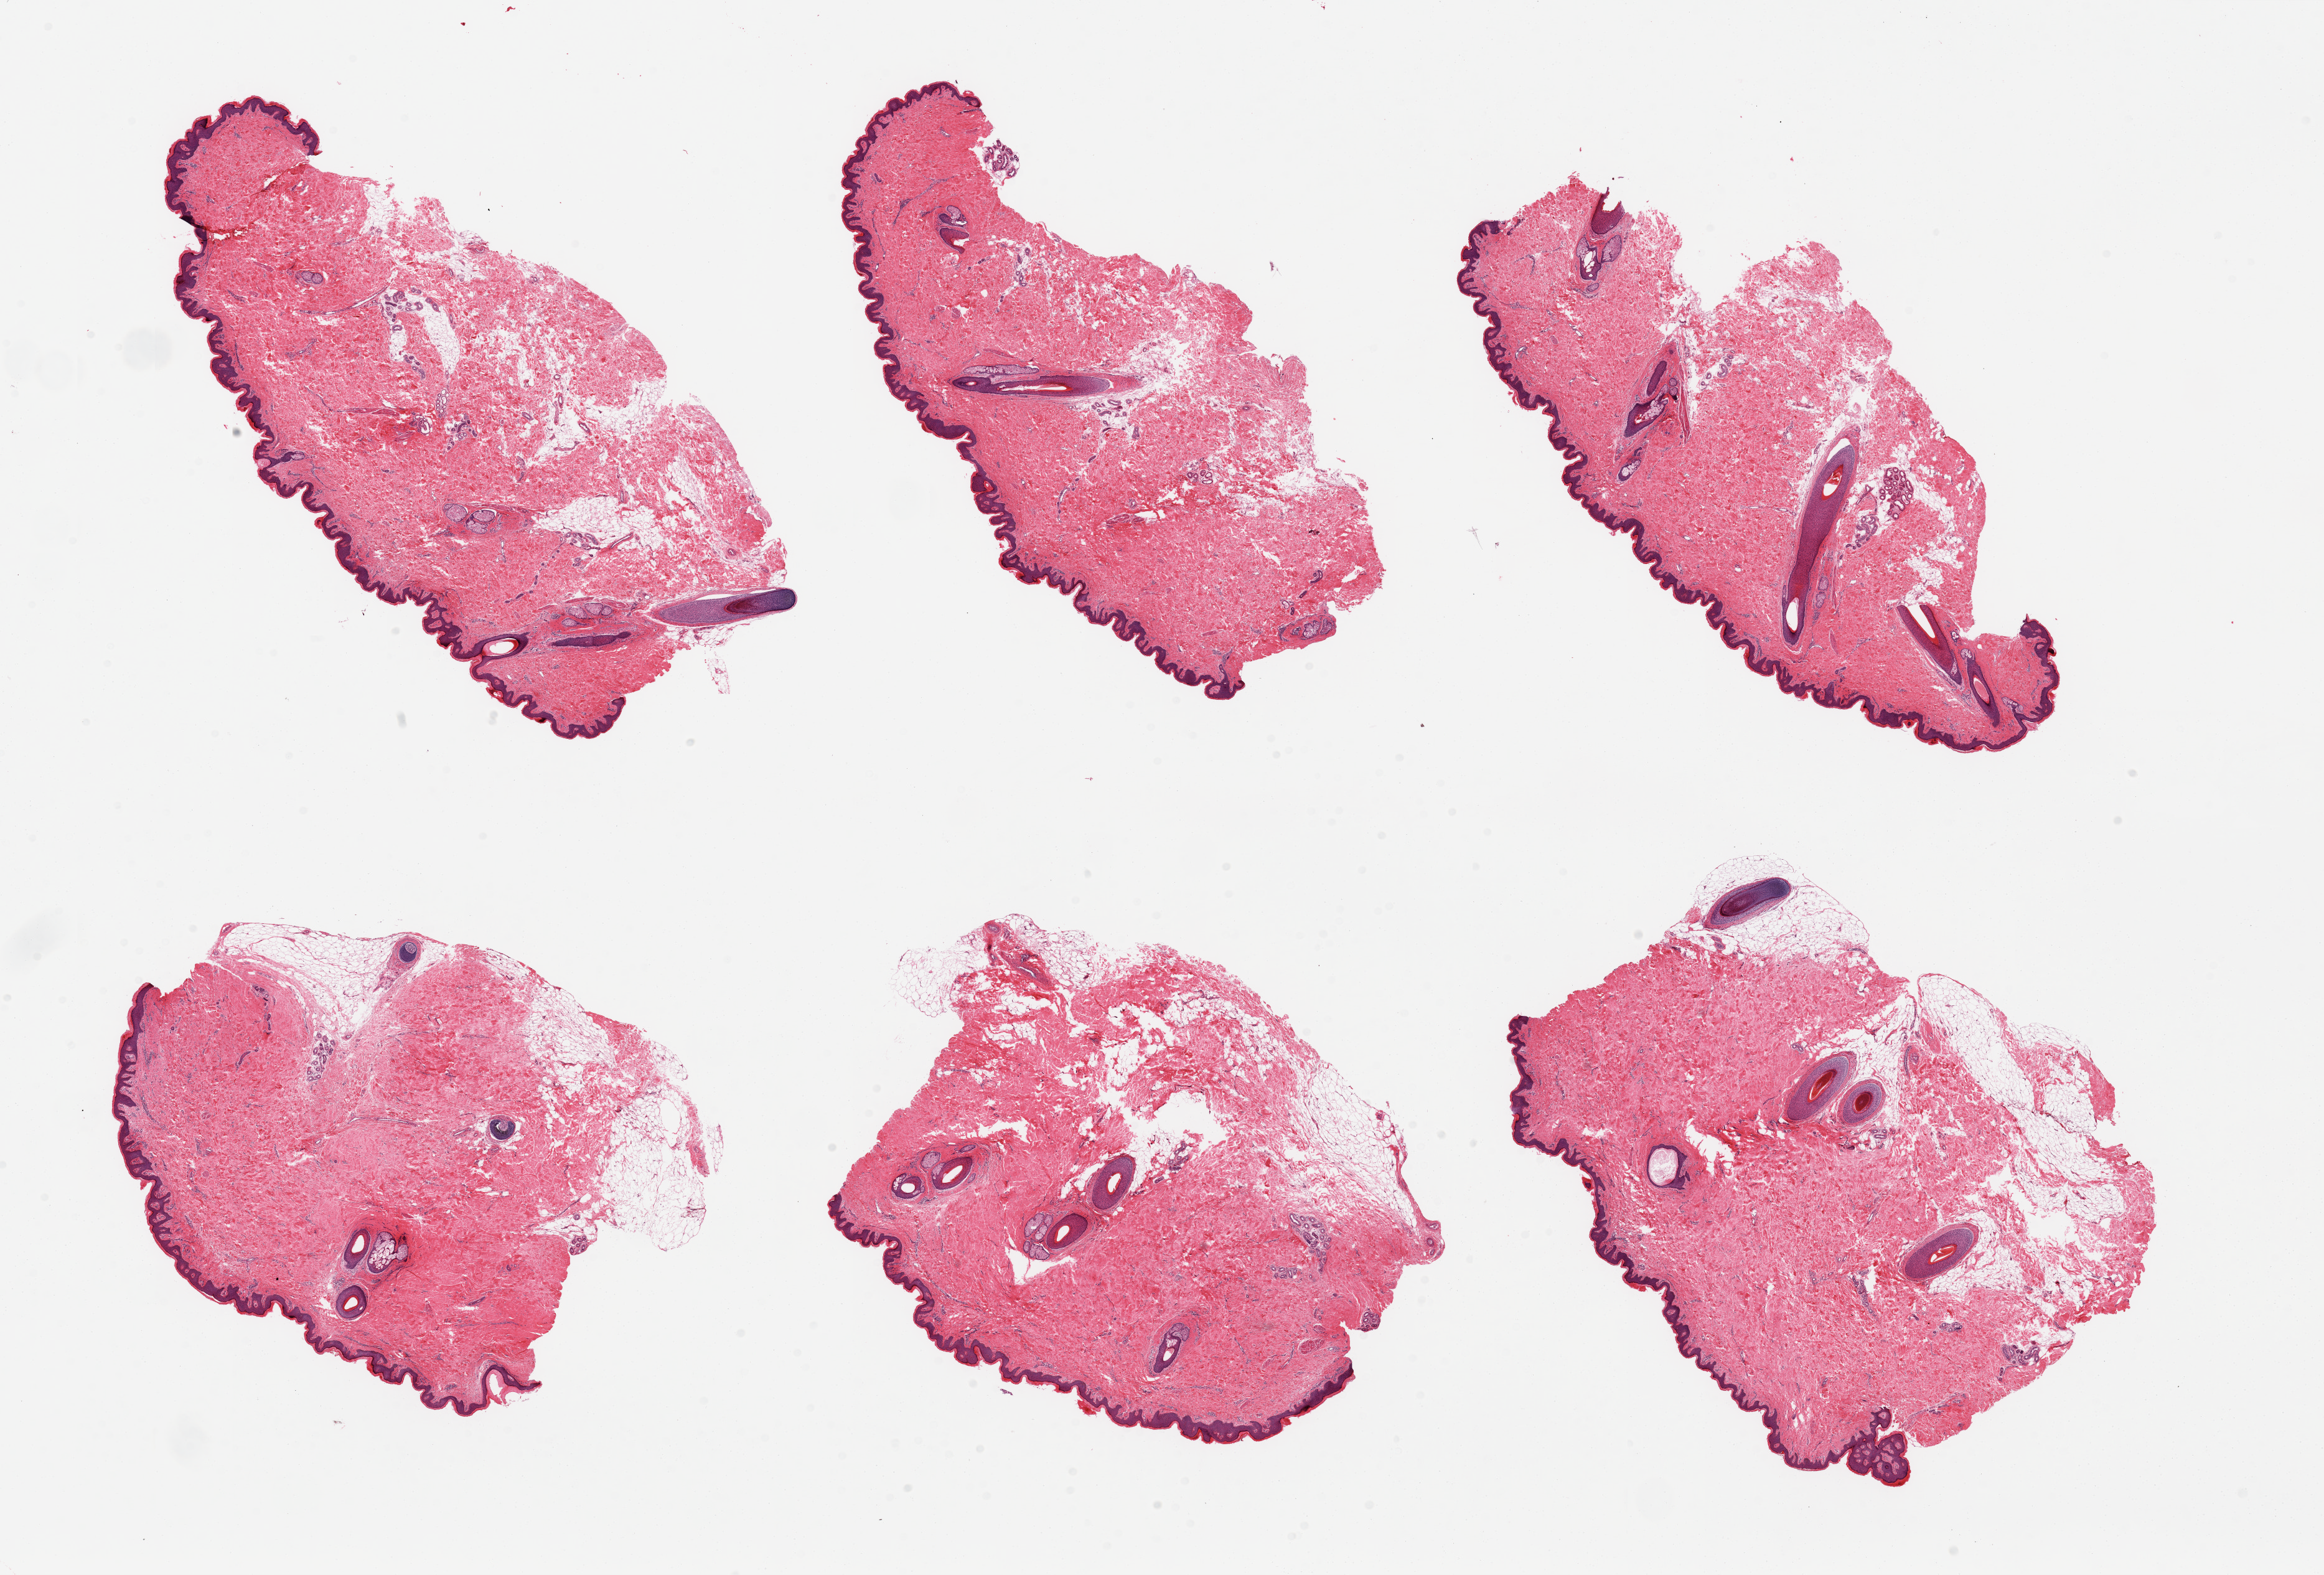
Digitized haematoxylin and eosin-stained section, brightfield, a low-resolution overview of the entire scanned area, about 29.5 x 20.0 mm. PAXgene-fixed, paraffin-embedded tissue. Target tissue: skin of suprapubic region. Donor tissue sample. Male donor.
- reviewer comment on this tissue sample: 6 pieces, trace dermal fat; squamous epithelium is ~70 microns